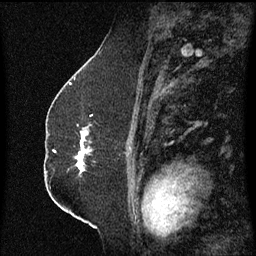
Breast MRI (dynamic contrast-enhanced), one sagittal slice; dynamic contrast-enhanced series, image 2 of 3 at this slice position (ordered by acquisition); 1.5 T; TE 4.2 ms, TR 8.4 ms; 256 × 256 image matrix. Female patient, age 52 years. Case-level facts recorded for this patient, not image findings: setting: breast cancer imaged before/during neoadjuvant chemotherapy; receptor status: HR-positive, HER2-negative.
Annotated regions visible in this slice (semi-automatic segmentation, software-assisted and operator-edited):
- analysis volume of interest (the breast-tissue region the enhancement analysis was run in; not a lesion): bounding box [x1, y1, x2, y2] px = [77, 124, 121, 179]
- tumour enhancement mask (voxels above the 70 % enhancement threshold inside the analysis volume of interest): [78, 132, 90, 171]